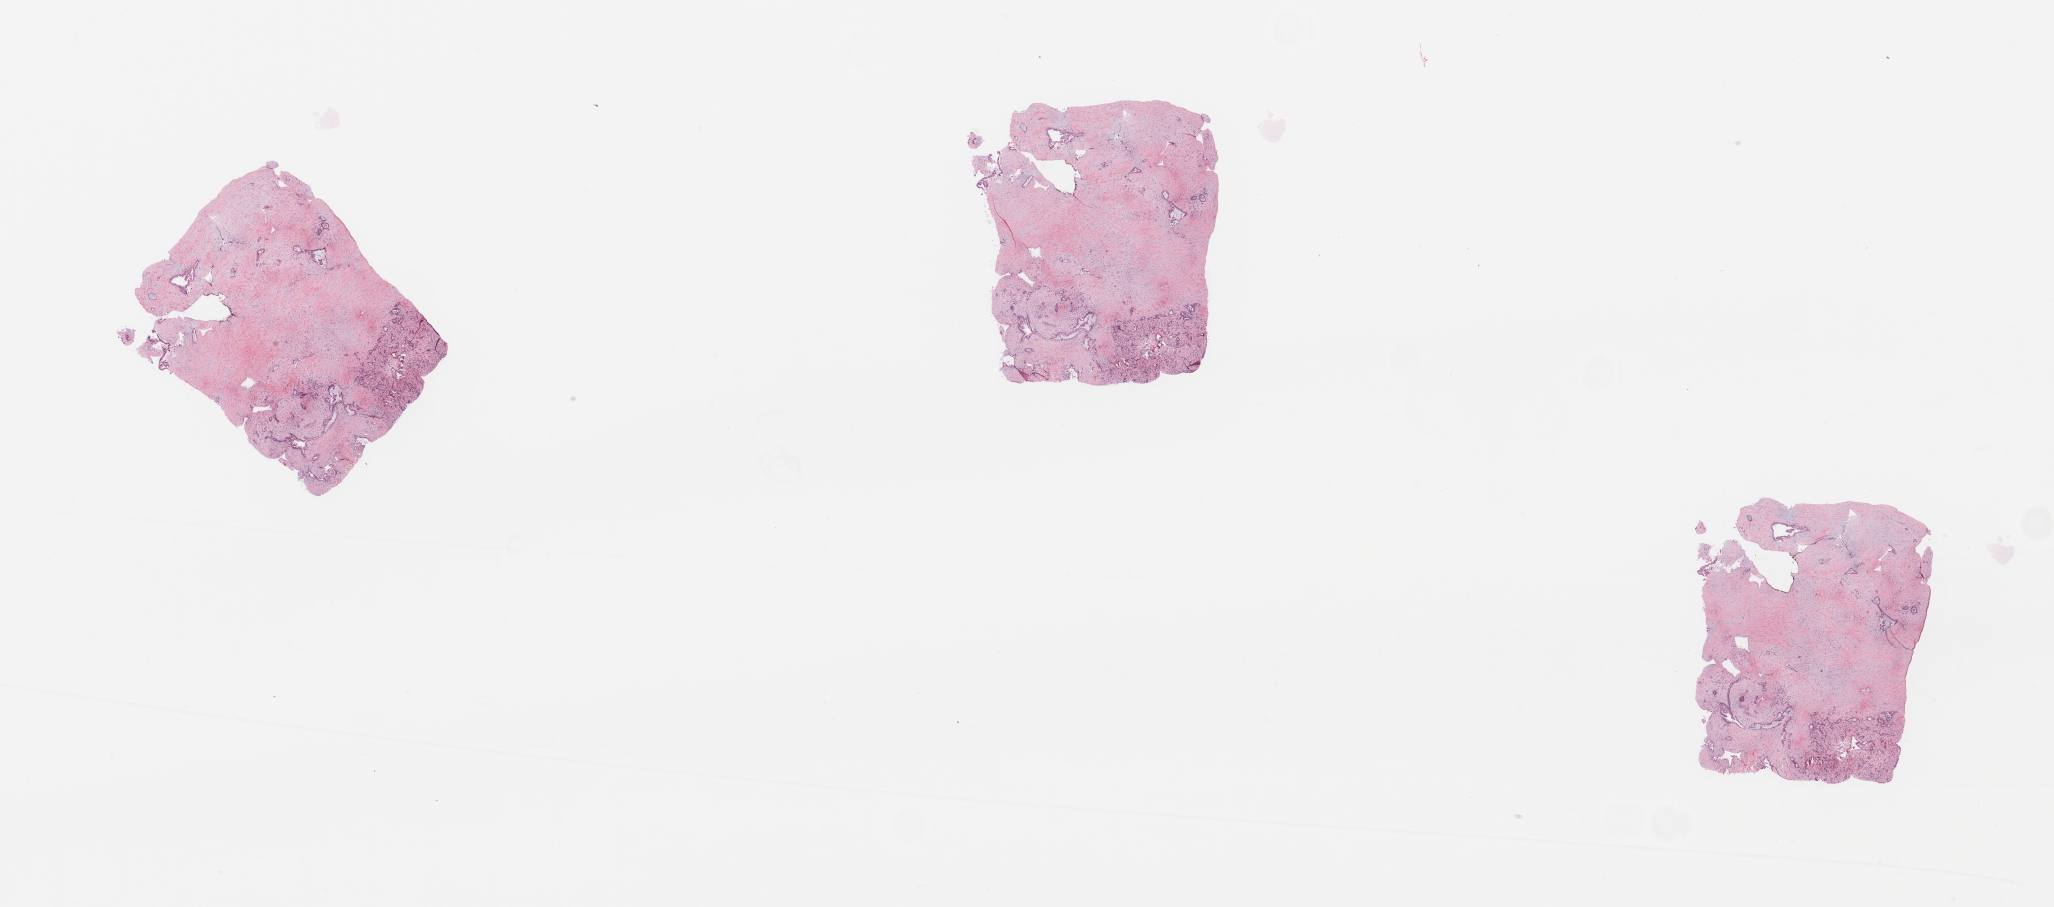
H&E whole-slide image — a low-resolution overview of the entire scanned area, about 32.5 x 14.3 mm (from a 20x scan), tumour tissue sample, sampled site: pancreas. Female, 79 y/o.
Diagnosis: Infiltrating duct carcinoma, NOS.